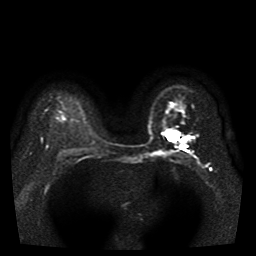
Breast MRI, one axial slice. Slice 31 of 41 in the series (ordered by position). Diffusion-weighted series; image 2 of 4 stored at this slice position (different b-values; order by instance number). 1.5 T. 256 × 256 image matrix, field of view 330 × 330 mm. Female patient.
Structures marked on this image (manually delineated by an expert):
- tumour on diffusion-weighted imaging: box from (x=177, y=137) to (x=185, y=146) px